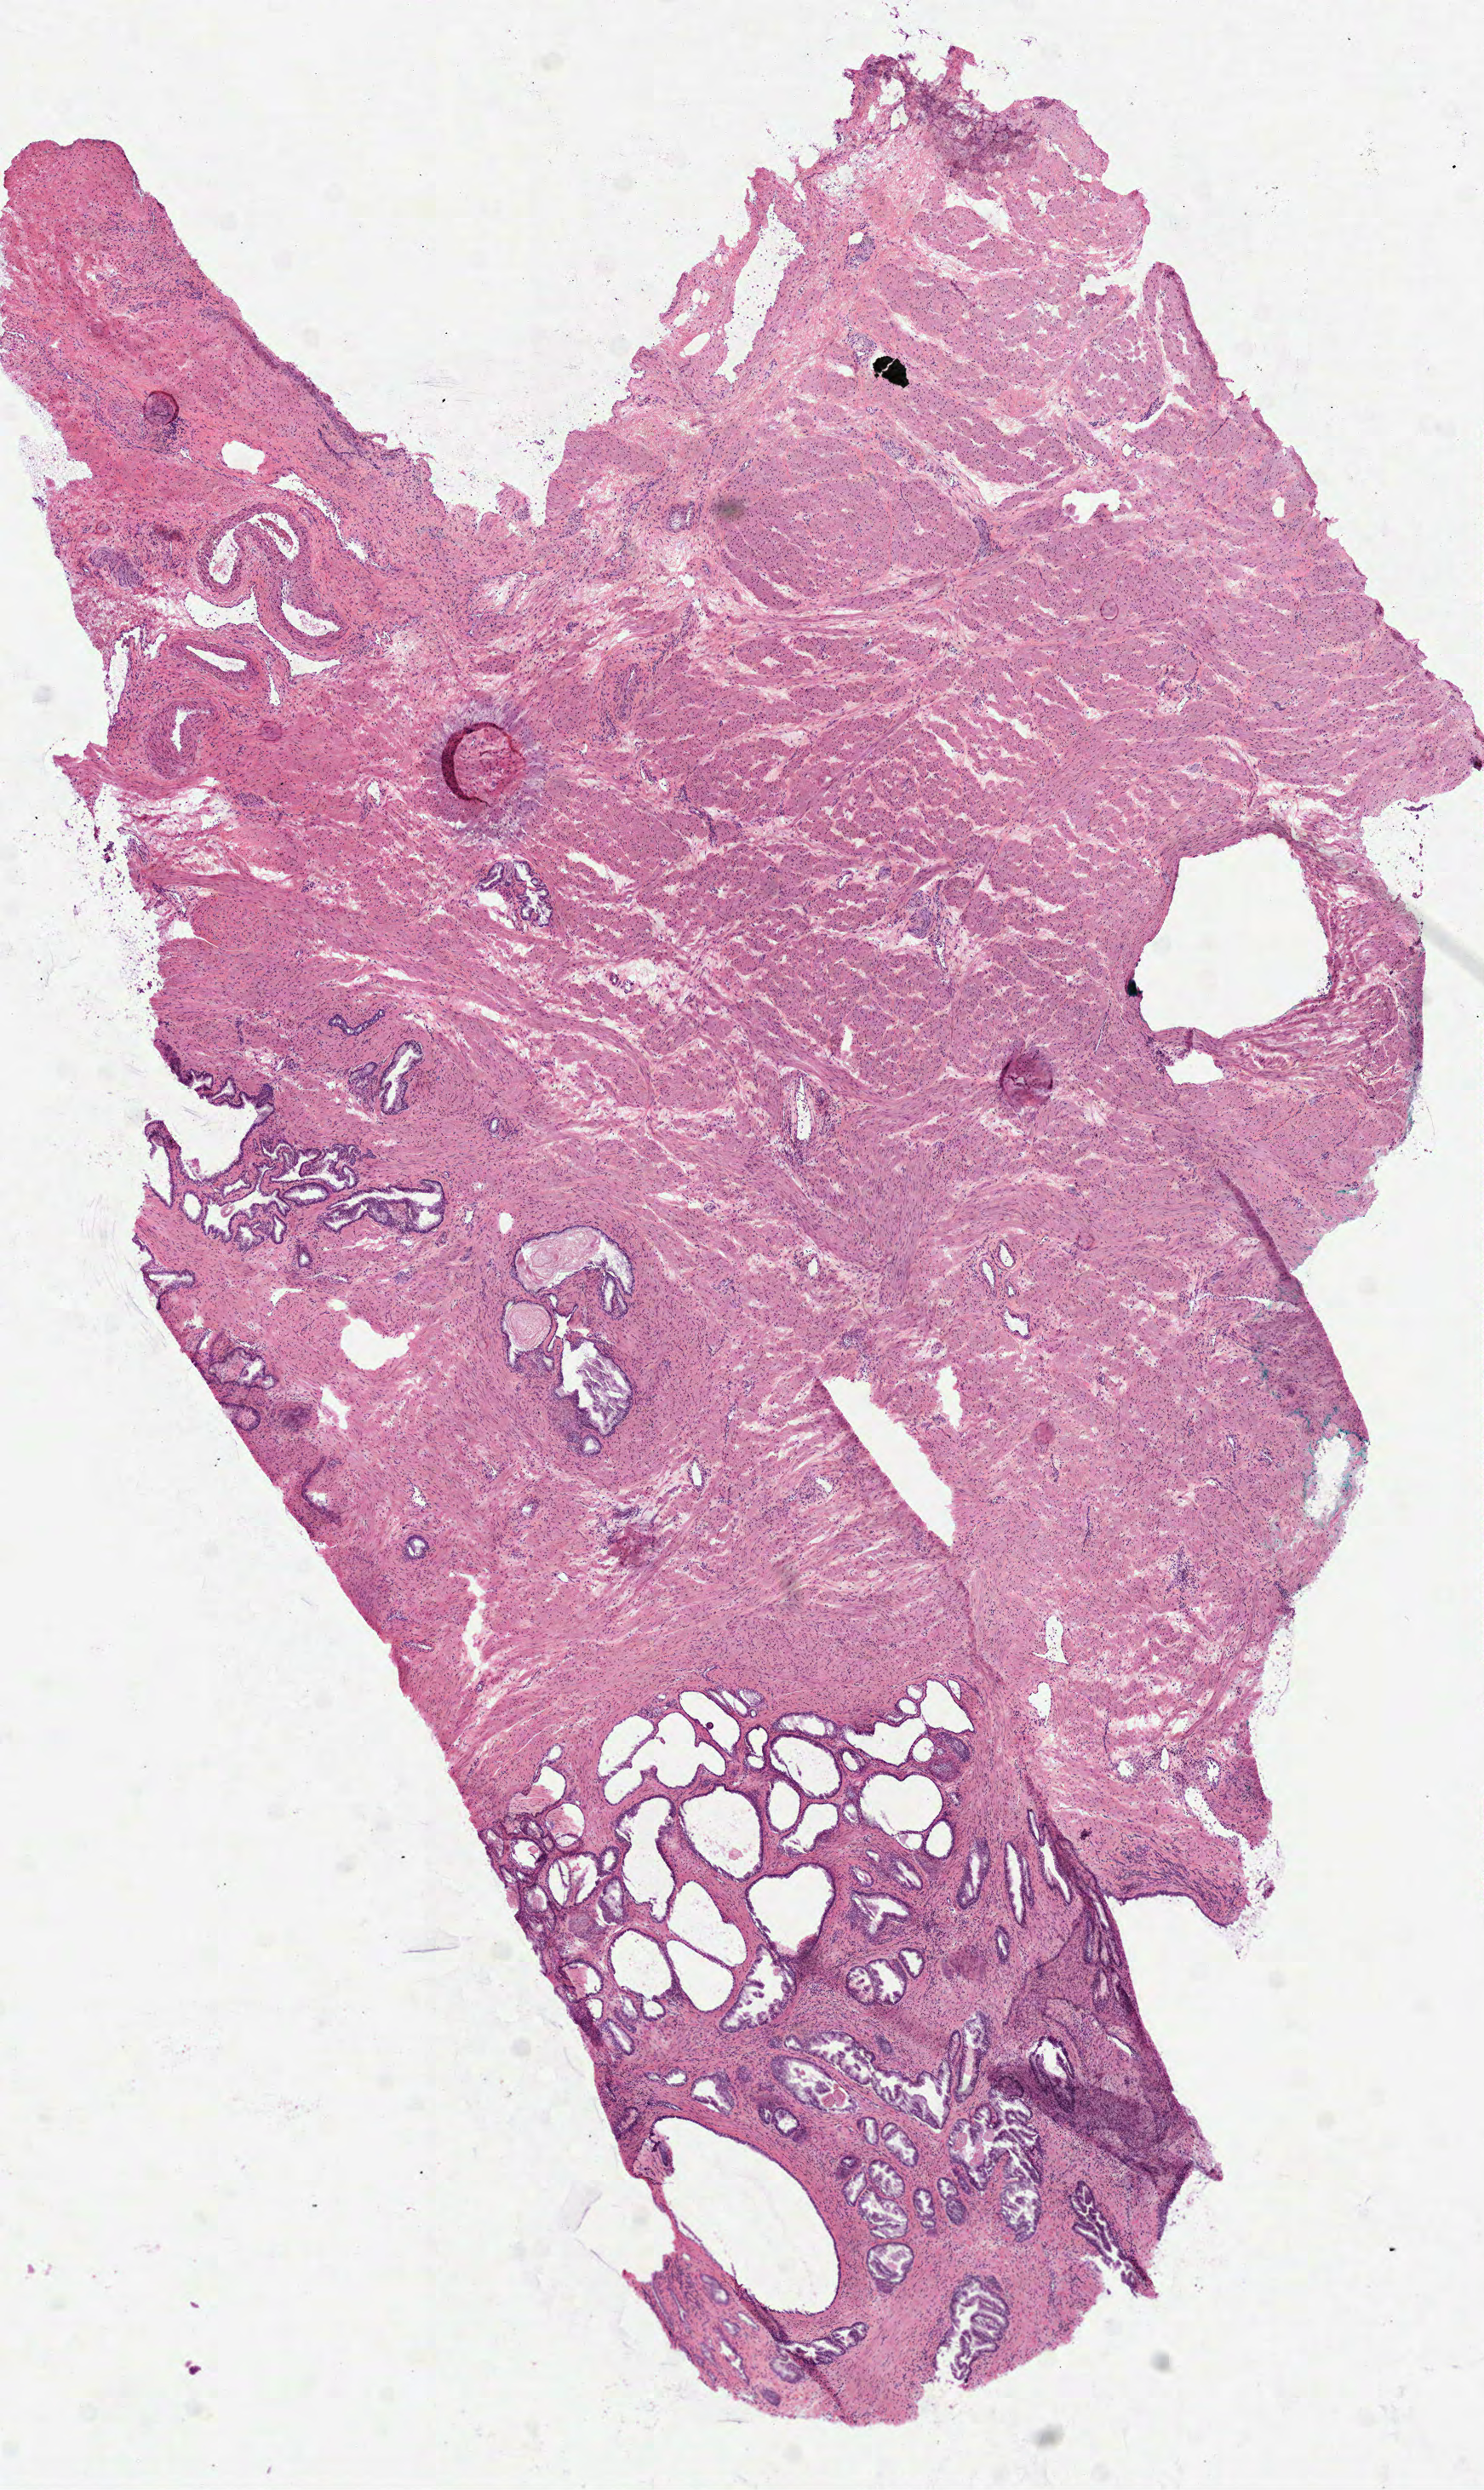
Whole-slide histology image, H&E-stained — whole scanned area (about 7.0 x 11.8 mm, acquisition: 40x scan) shown as a low-resolution overview; frozen section; sample: solid tissue normal (non-tumour tissue), prostate. Patient: male, age at initial diagnosis 66 years.
This section: solid tissue normal sample (biorepository sample class). Patient diagnosis: Acinar cell carcinoma (prostate gland).